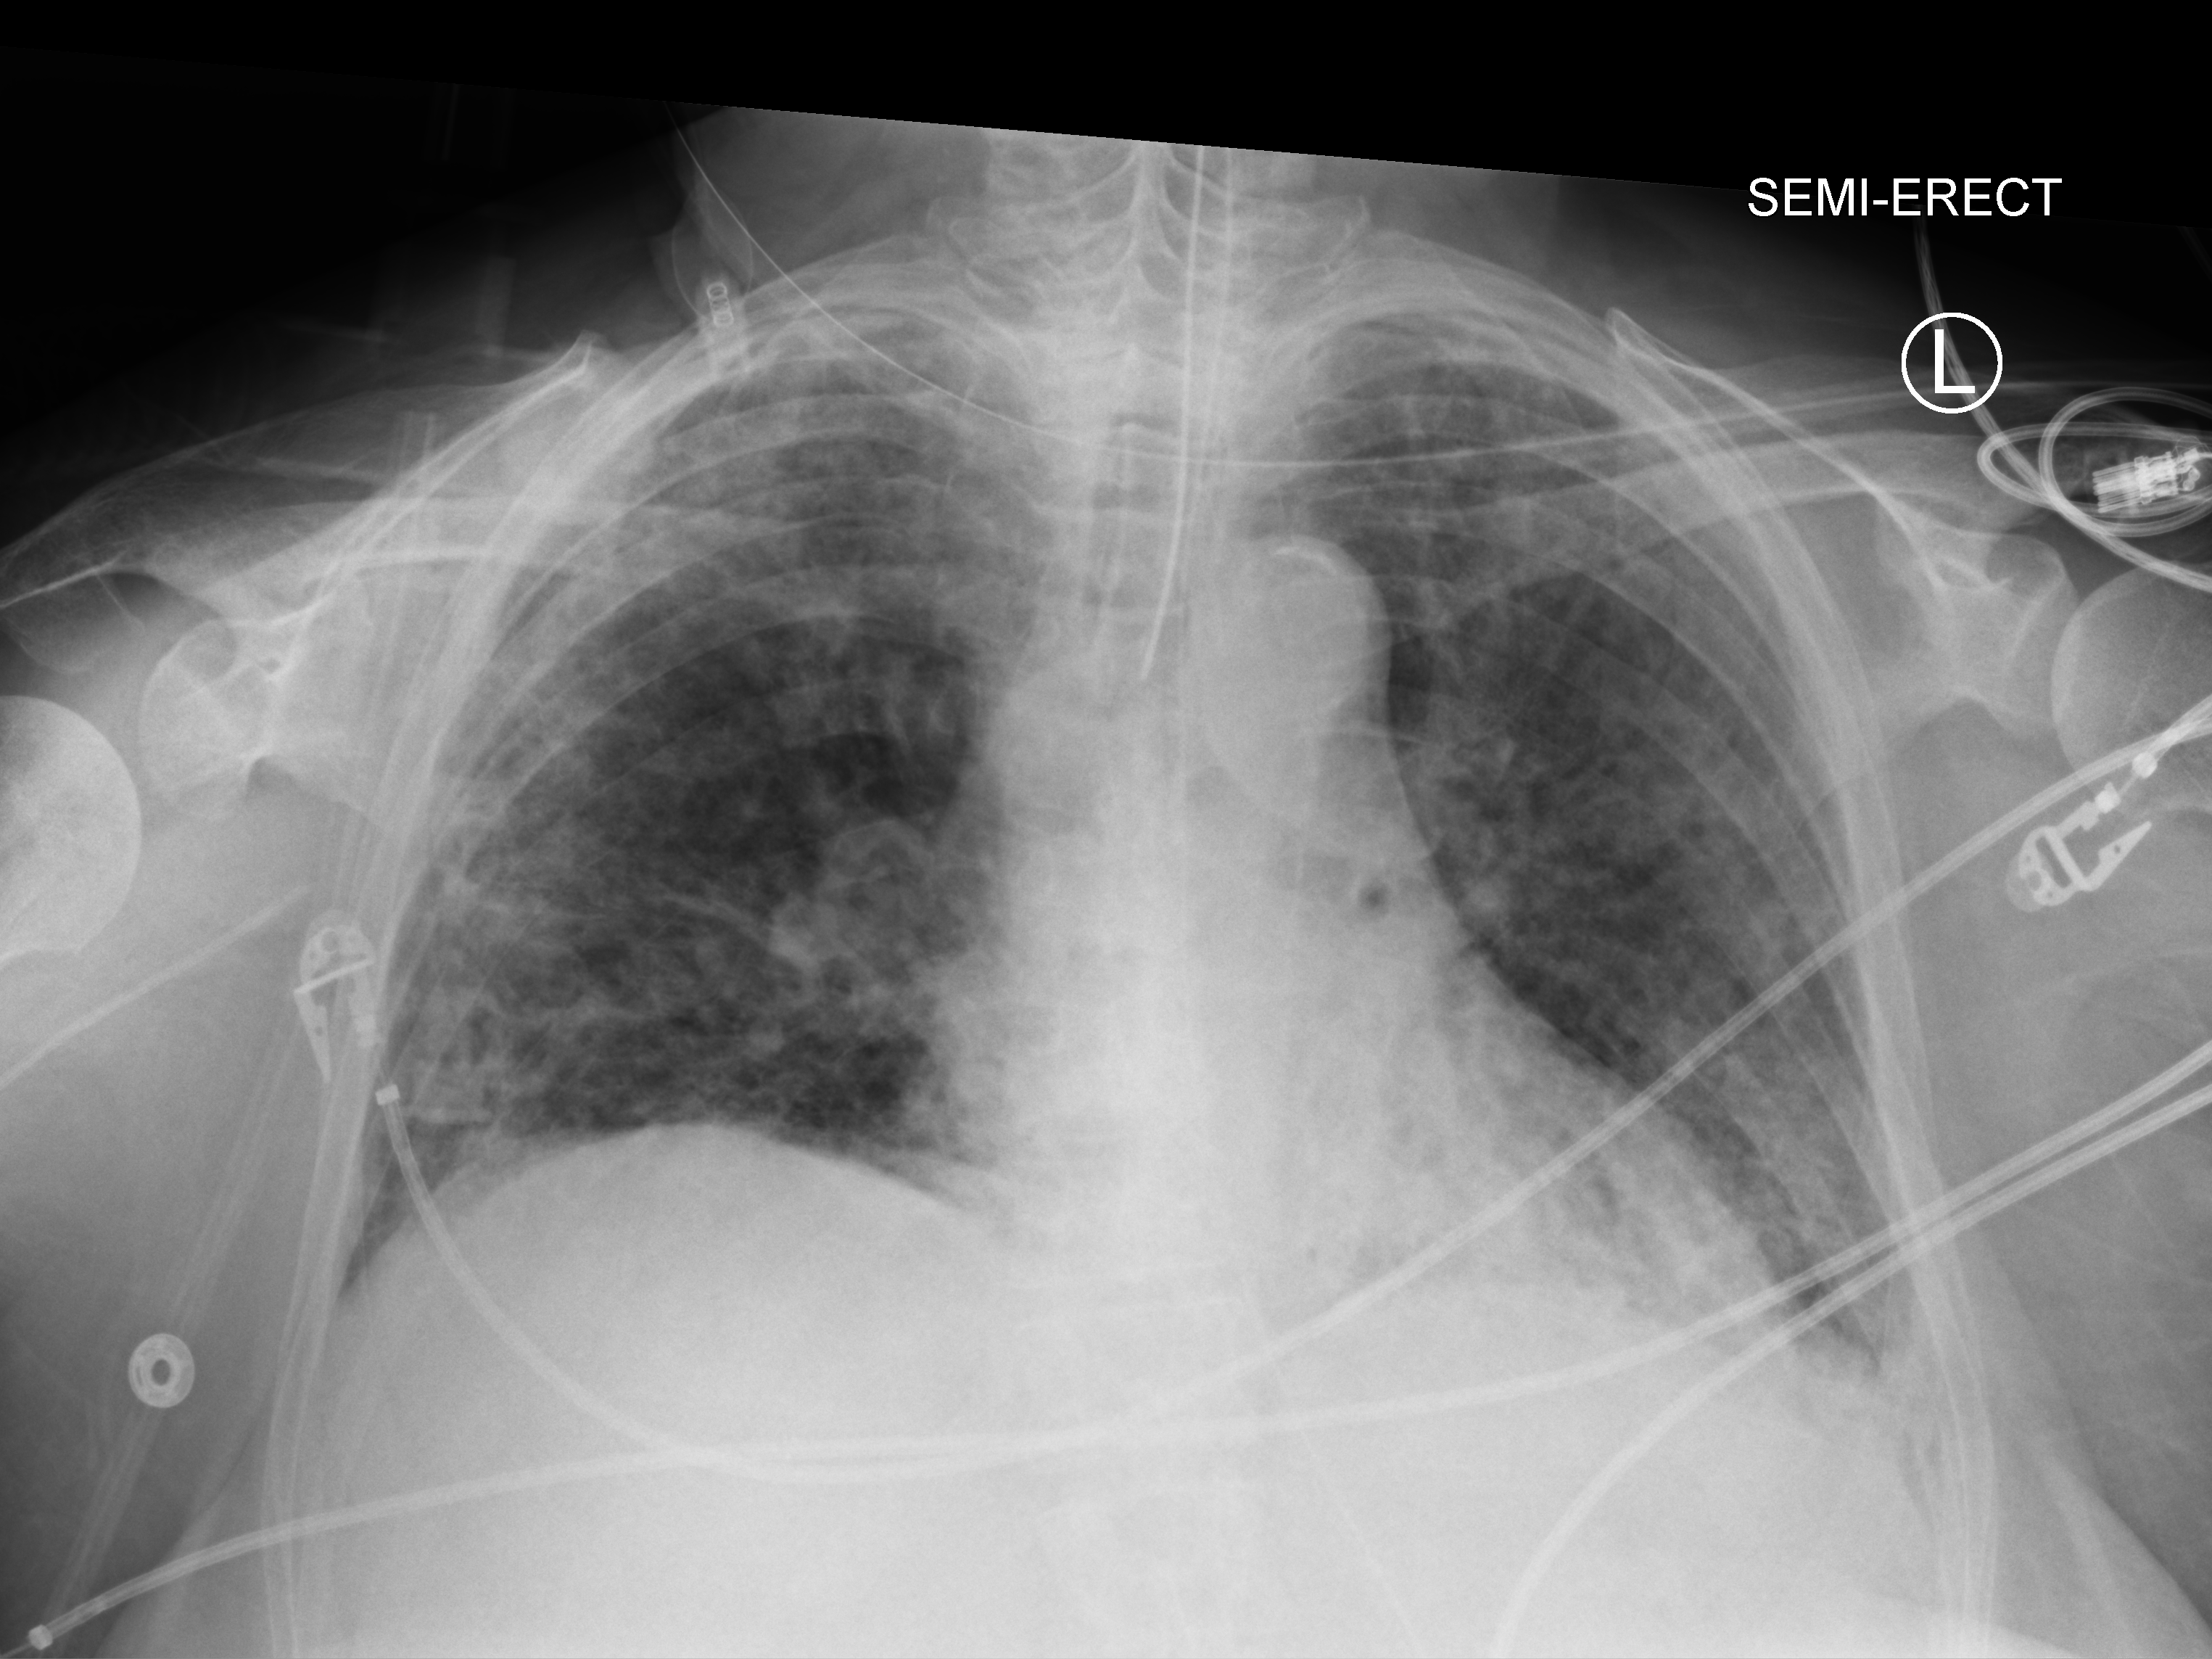
Bedside chest radiograph (computed radiography), anteroposterior (AP) projection. Female patient hospitalised with COVID-19, age 75–90 years.
Admission-level facts for this patient (not findings on this image; timing relative to this image not recorded): mechanically ventilated during this hospital stay: yes.